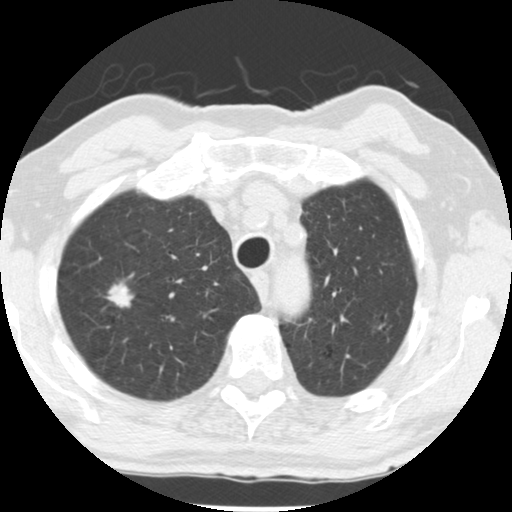
Low-dose screening chest CT, one axial slice. Slice 204 of 252 in the series (ordered by position). 120 kVp. Lung window (W 1500 / L -600 HU). 512 × 512 image matrix.
Structures marked on this image (outlined manually by an expert reader):
- lesion 1 (tumor, upper lobe of right lung): bounding box (x1, y1, x2, y2) in pixels: (105, 280, 134, 308)